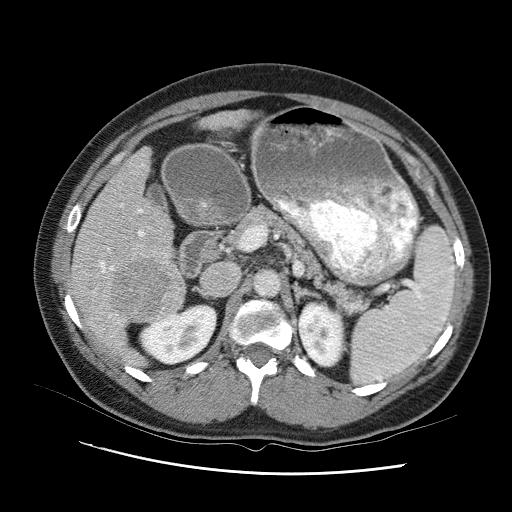
Contrast-enhanced abdominal CT (liver protocol), one axial slice; slice 48 of 95 in the series (ordered by position); 120 kVp; one of 2 acquisitions stored at this slice position; soft-tissue window (W 400 / L 40 HU); 512 × 512 image matrix, field of view 360 × 360 mm. Case-level facts recorded for this patient, not image findings: diagnosis: hepatocellular carcinoma (patient treated with transarterial chemoembolisation; whether this scan precedes or follows treatment is not stated here); TNM stage (as recorded): Stage-I; Child-Pugh class: B; tumour differentiation: moderately differentiated; tumour nodularity: uninodular.
Outlined on this slice (semi-automatically segmented with operator editing):
- liver parenchyma outside the tumour (the mass and vessels are separate outlines, so this box may not span the whole liver): bounding box <68,107,250,368> (left, top, right, bottom; pixels)
- mass: <114,251,189,316>
- liver vessels: <108,166,185,322>